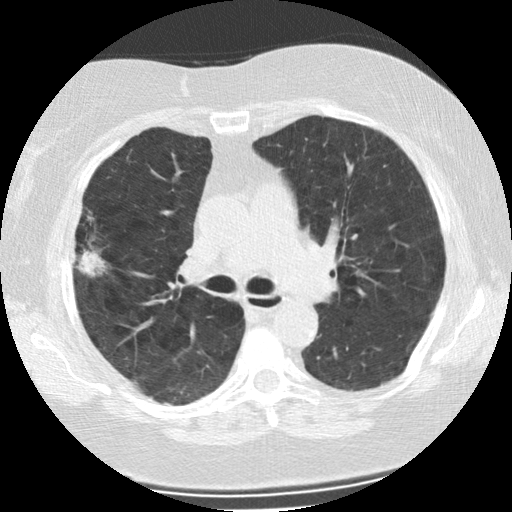
Chest CT (low-dose screening protocol), one axial image, second screening round (one year after baseline), lung window (W 1500 / L -600 HU), slice 82 of 225 in the series. Female participant, aged 73 years at enrolment. Former smoker at enrolment.
Expert reader's lesion annotation, bounding box (x1, y1, x2, y2) in pixels: (54, 216, 111, 287). The screening reader recorded 2 non-calcified nodules or masses ≥4 mm on this exam (right upper lobe, left upper lobe); which of them this box marks is not recorded. Lung cancer was diagnosed 47 days after this screen: bronchiolo-alveolar adenocarcinoma, NOS, right upper lobe, moderately differentiated (G2), stage IIIB (AJCC 6th edition), 21 mm at pathology.